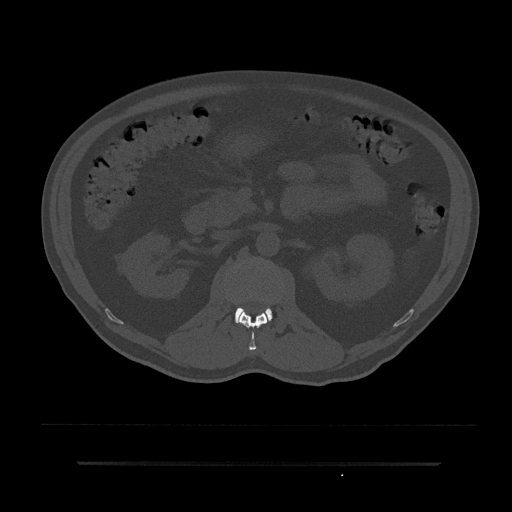
CT including the spine, one axial slice. Slice 112 of 797 in the series (ordered by position). Bone window (W 1800 / L 400 HU). 0.5 mm slice thickness. 512 × 512 image matrix. Patient: male, 59 years. From the clinical record (not read from this slice): primary cancer: bile ducts; vertebrae with lytic lesions (as recorded): T10.
Annotated regions visible in this slice (semi-automatically segmented with operator editing):
- L1 vertebra: bounding box [x1, y1, x2, y2] px = [238, 312, 268, 352]
- L2 vertebra: [235, 308, 272, 323]